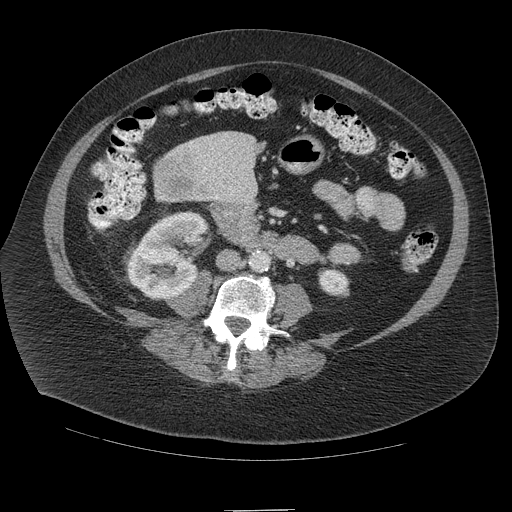
Contrast-enhanced abdominal CT (liver protocol), one axial slice. Position 25 of 109 along the scan axis. Reconstruction kernel STANDARD. 140 kVp. Soft-tissue window (W 400 / L 40 HU). 512 × 512 image matrix. From the clinical record (not read from this slice): diagnosis: hepatocellular carcinoma (patient treated with transarterial chemoembolisation; whether this scan precedes or follows treatment is not stated here); TNM stage (as recorded): Stage-IVB; Child-Pugh class: A; tumour differentiation: poorly differentiated; tumour nodularity: multinodular.
Structures marked on this image (semi-automatically segmented with operator editing):
- liver parenchyma outside the tumour (the mass and vessels are separate outlines, so this box may not span the whole liver): bounding box <206,131,258,166> (left, top, right, bottom; pixels)